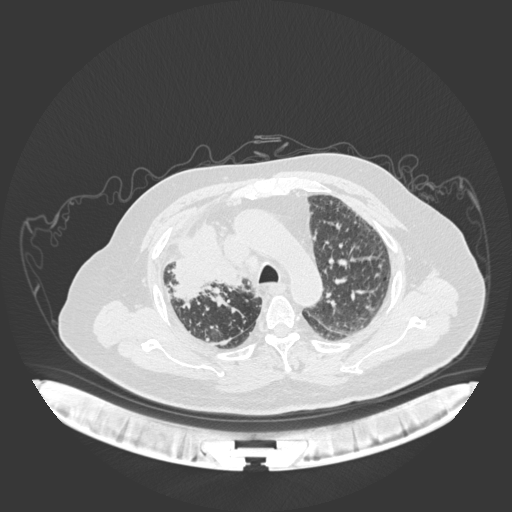
Chest CT, one axial slice. Position 134 of 201 along the scan axis. Reconstruction kernel B30f. Lung window (W 1500 / L -600 HU). 1 mm slice thickness. 512 × 512 image matrix, field of view 500 × 500 mm. Patient: male, 69 years. Case-level facts recorded for this patient, not image findings: clinical TNM (as recorded): T4 N3 M1.
Annotated regions visible in this slice (rectangle marked by the reading radiologist):
- lung tumour (recorded histology: adenocarcinoma): box from (x=169, y=217) to (x=251, y=304) px